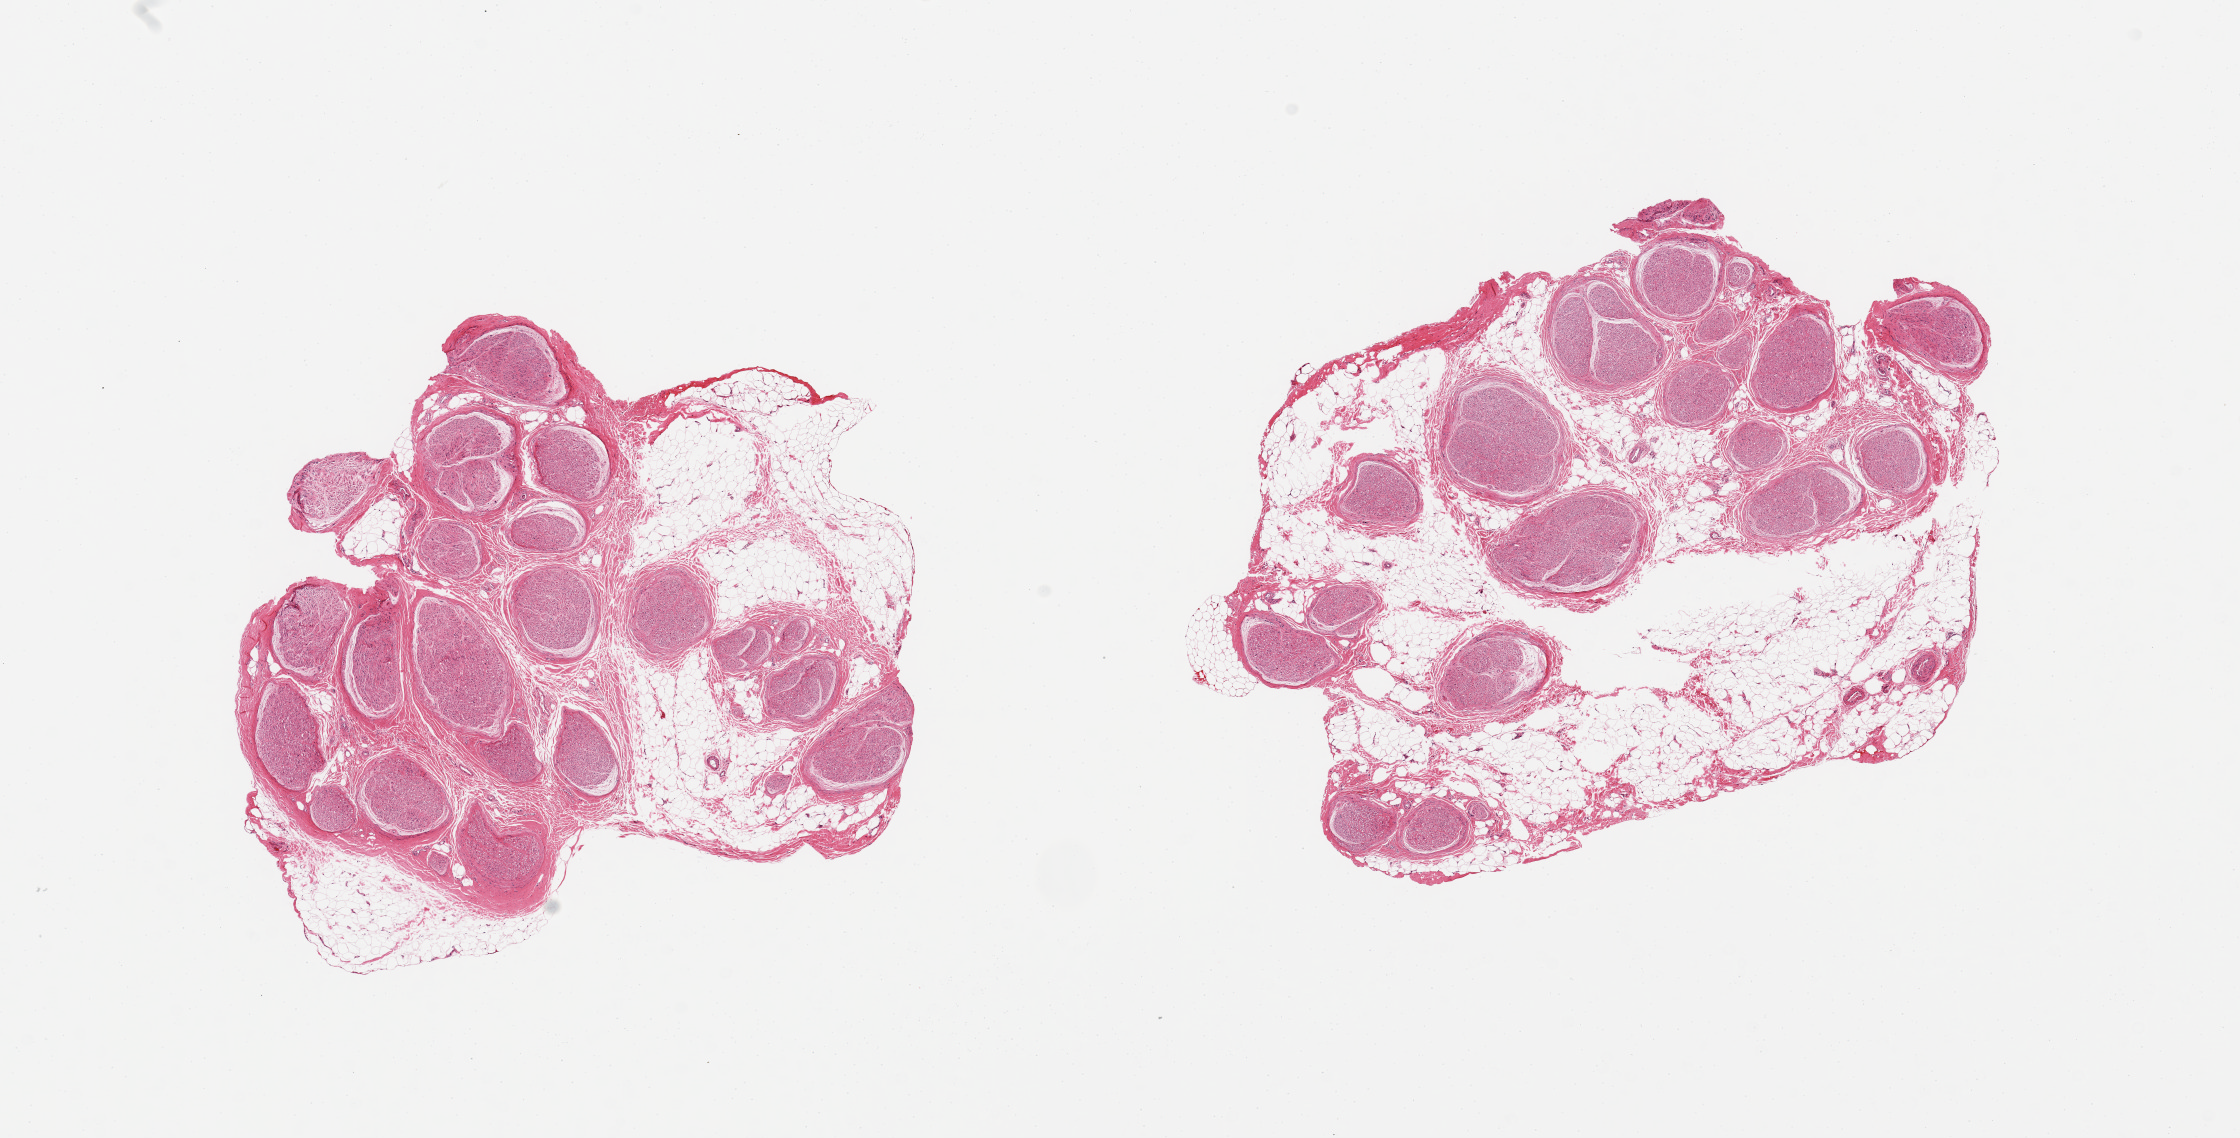
Whole-slide image, haematoxylin and eosin stain, shown as a low-resolution overview of the whole scanned area (about 17.7 x 9.0 mm, acquisition: 20x scan); PAXgene-fixed, paraffin-embedded tissue; sampled site (target tissue): tibial nerve; donor tissue sample.
Review note (as recorded): 2 pieces, ~40% interstitial/adherent fat.